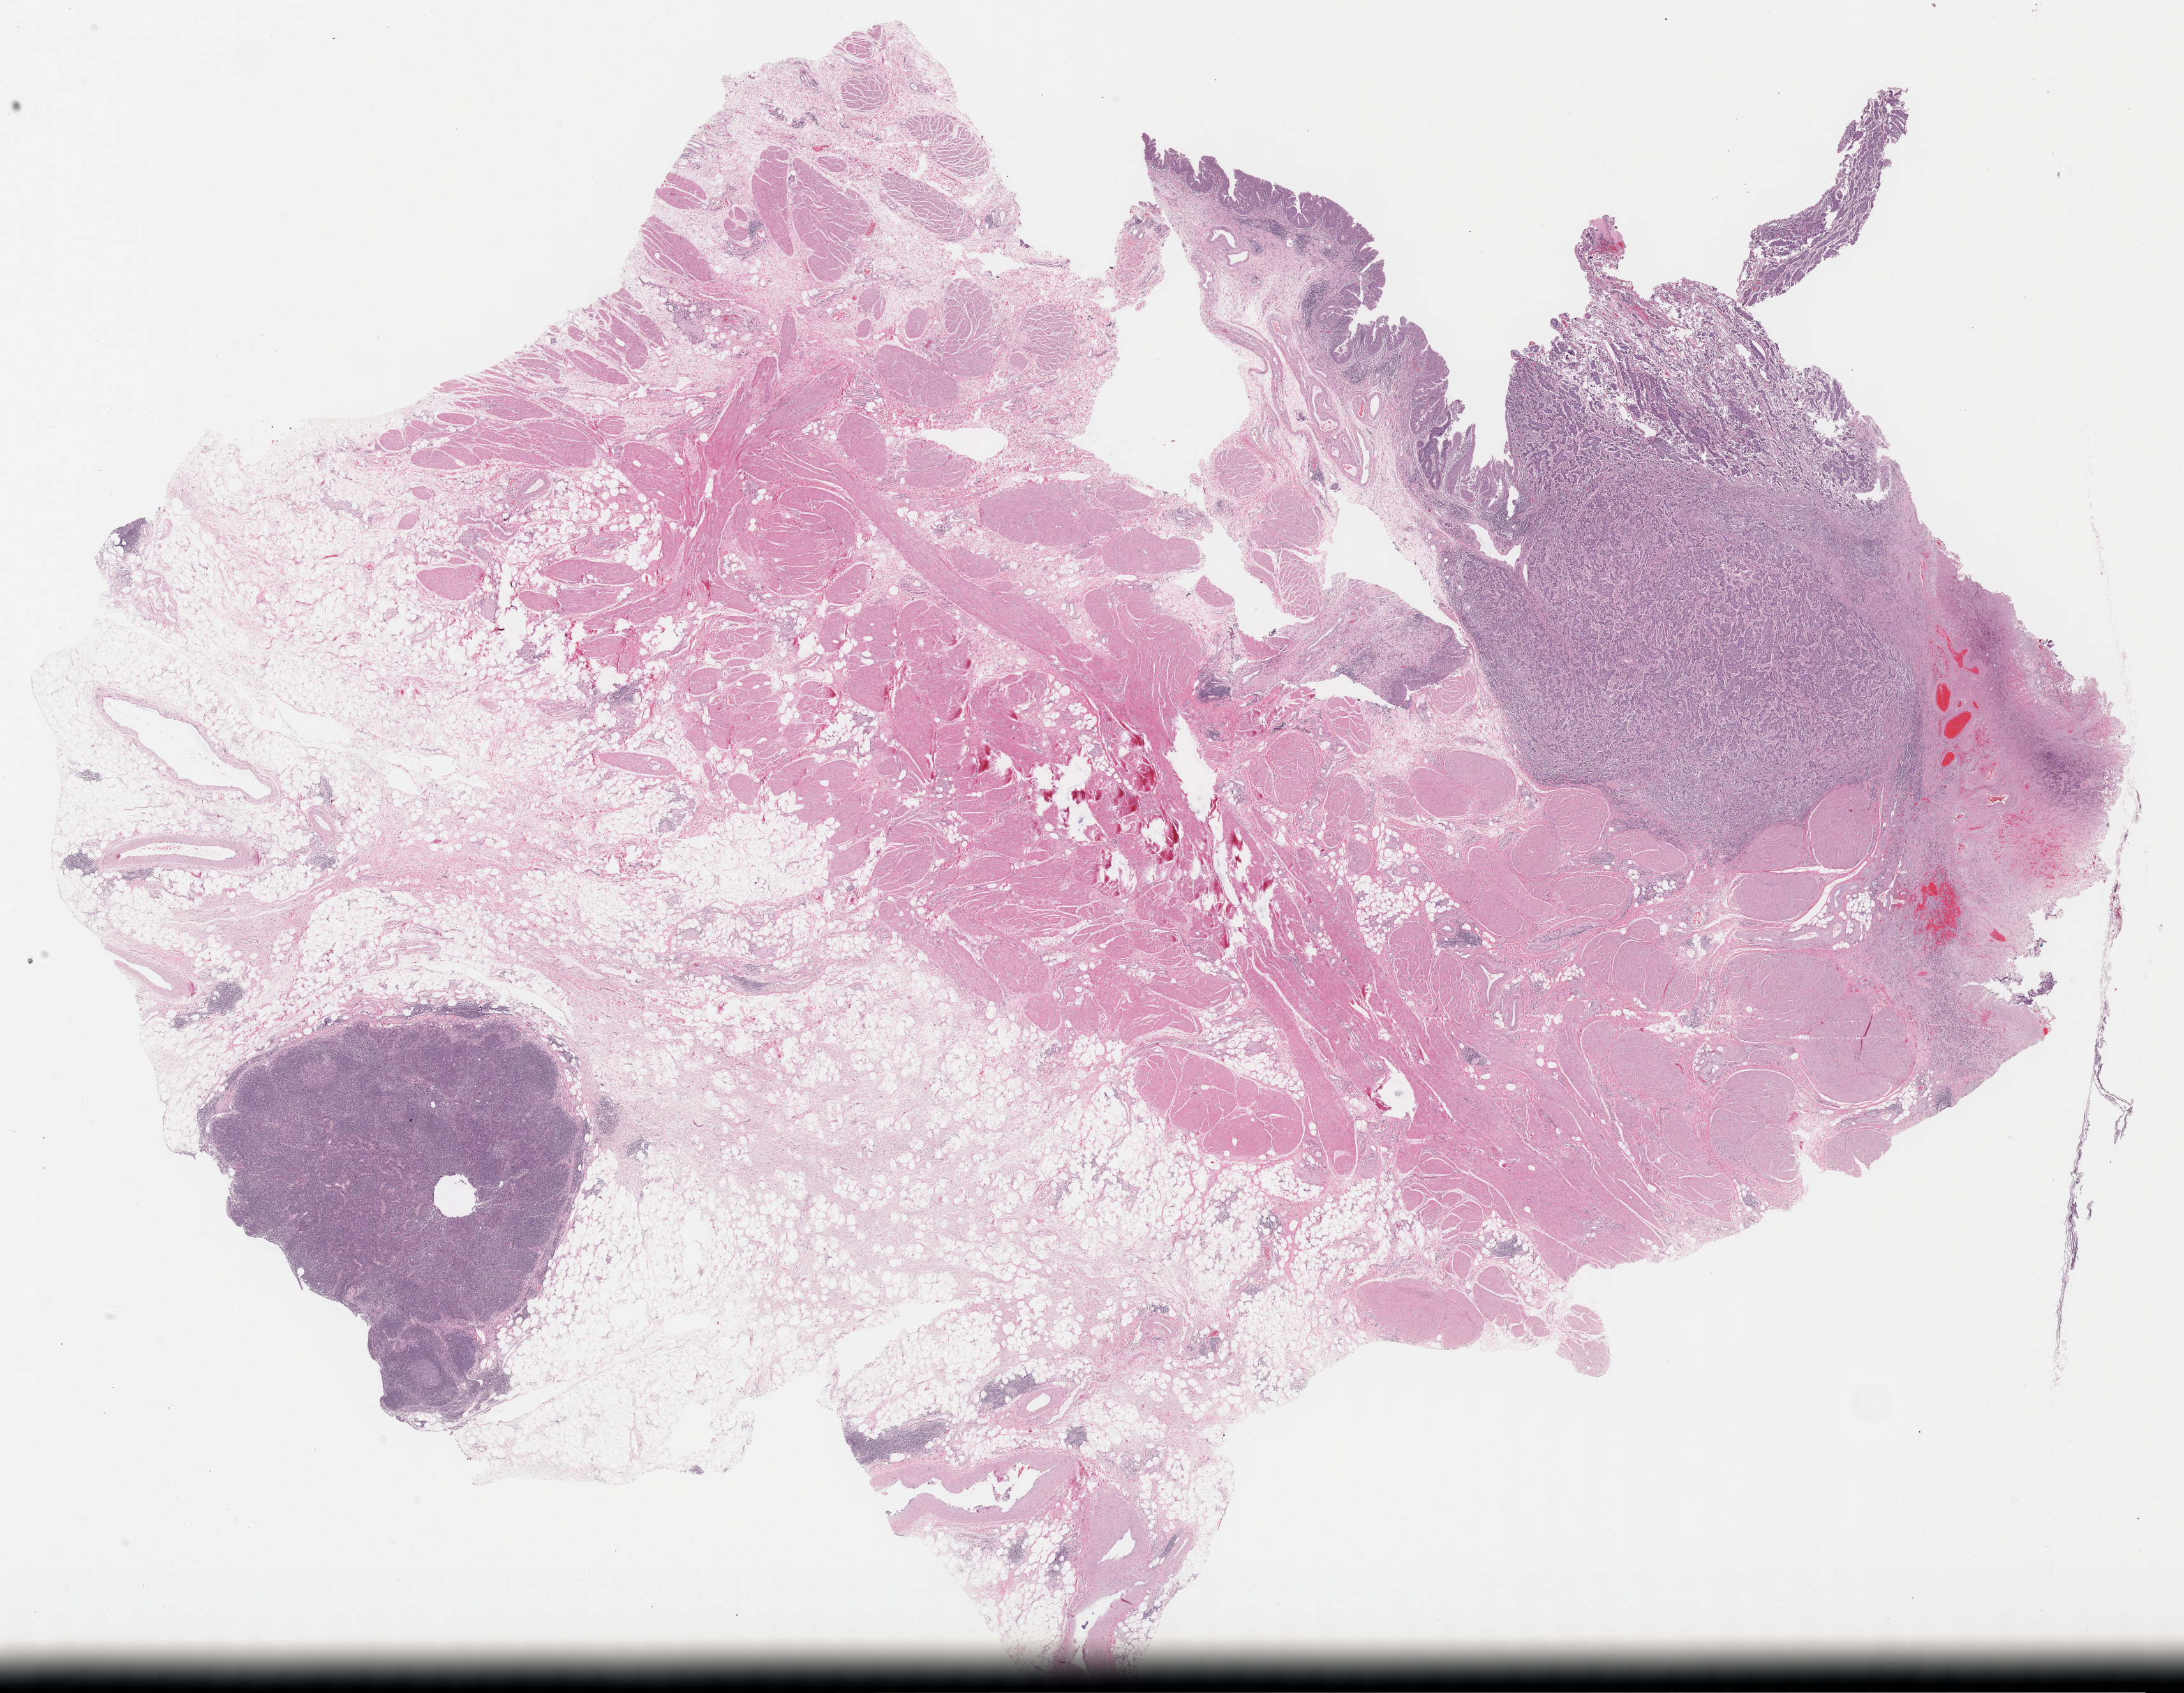
Digitized Hematoxylin and eosin (H&E) stained tissue section (whole slide), whole scanned area (about 27.7 x 21.5 mm, slide scanned at 40x) shown as a low-resolution overview, formalin-fixed paraffin-embedded (FFPE) diagnostic section, bladder, primary tumour sample. Male patient; age at initial diagnosis 53 years. Histologic grade: high grade.
Pathologic diagnosis: Transitional cell carcinoma. Lymph nodes positive (case pathology): 1 of 40 examined. AJCC pathologic stage: IV (6th edition). TNM: T2a N1 M0.